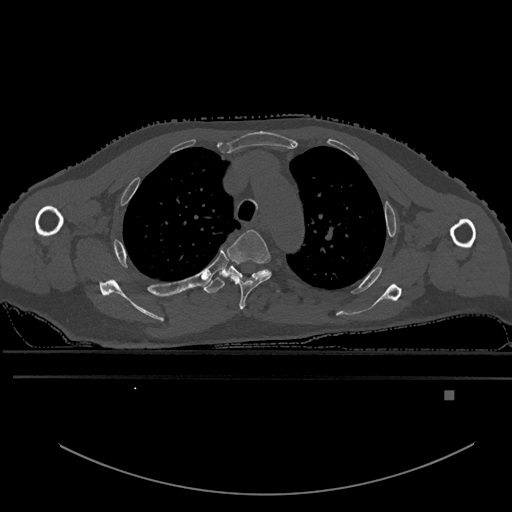
CT including the spine, one axial slice. Slice 434 of 969 in the series (ordered by position). Bone window (W 1800 / L 400 HU). 0.5 mm slice thickness. 512 × 512 image matrix, field of view 456 × 456 mm. Patient: male, 82 years. Case-level facts recorded for this patient, not image findings: primary cancer: prostate.
Annotated regions visible in this slice (semi-automatic segmentation, software-assisted and operator-edited):
- T3 vertebra: box from (x=227, y=230) to (x=272, y=310) px
- T4 vertebra: (x=203, y=263)–(x=280, y=294)